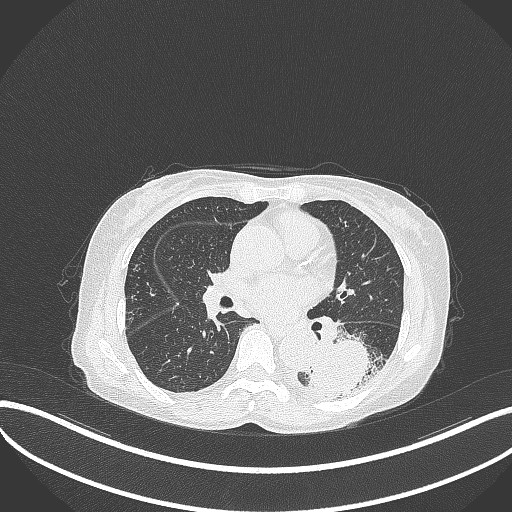
Chest CT, one axial slice; position 159 of 370 along the scan axis; 120 kVp; lung window (W 1500 / L -600 HU); 1 mm slice thickness; 512 × 512 image matrix, field of view 400 × 400 mm. Female patient, age 78 years. Case-level facts recorded for this patient, not image findings: clinical TNM (as recorded): T3 N0 M1.
Annotated regions visible in this slice (rectangle marked by the reading radiologist):
- lung tumour (recorded histology: squamous cell carcinoma): bounding box <308,339,387,396> (left, top, right, bottom; pixels)